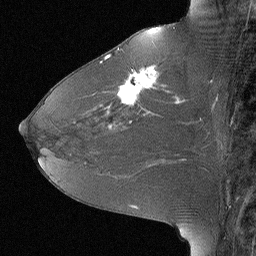
Breast MRI (dynamic contrast-enhanced), one sagittal slice; slice 34 of 64 in the series (ordered by position); dynamic contrast-enhanced study with each time point stored as its own series, time point 2 of 3 at this slice position (early post-contrast, ordered by acquisition time); 1.5 T; TE 4 ms, TR 30 ms; 256 × 256 image matrix, field of view 180 × 180 mm. Patient: female, 46 years. From the clinical record (not read from this slice): setting: breast cancer imaged before/during neoadjuvant chemotherapy; receptor status: HR-positive, HER2-negative.
Structures marked on this image (semi-automatic segmentation, software-assisted and operator-edited):
- analysis volume of interest (the breast-tissue region the enhancement analysis was run in; not a lesion): bounding box (x1, y1, x2, y2) in pixels: (106, 43, 184, 119)
- tumour enhancement mask (voxels above the 90 % enhancement threshold inside the analysis volume of interest): (109, 55, 179, 105)